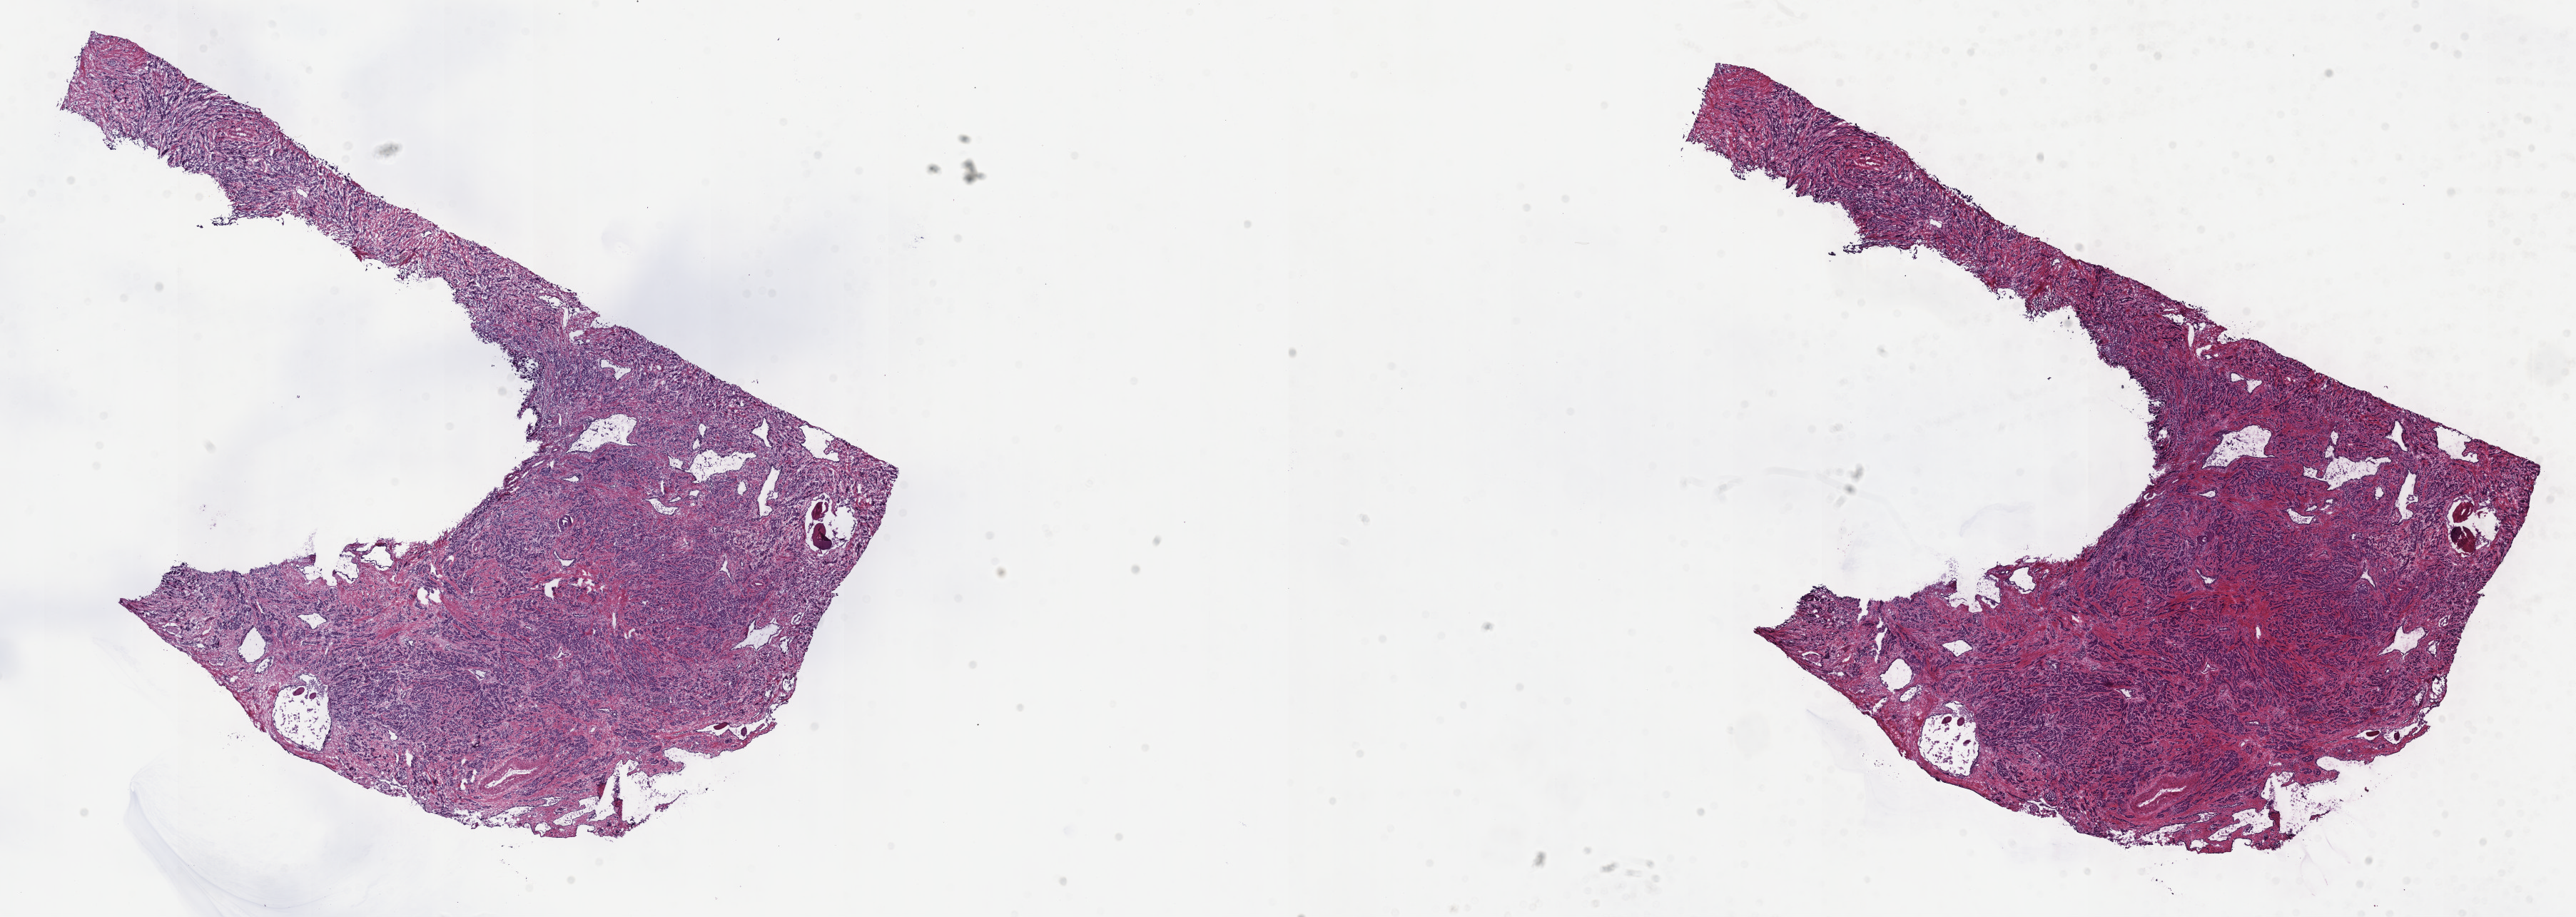
Whole-slide histology image, H&E-stained — whole scanned area (about 29.2 x 10.4 mm, from a 40x scan) shown as a low-resolution overview, frozen section from the top of the tissue portion, primary tumour sample from the prostate. Patient: male, age at initial diagnosis 62 years. Gleason score: 8 (4+4). Pathologist review of this section (percent, as recorded): tumour cells 95%, tumour nuclei 70%, normal cells 5%, stromal cells 0%, necrosis 0%. Infiltration values recorded for this section: lymphocyte infiltration 0%, monocyte infiltration 0%, neutrophil infiltration 0%.
Diagnosis: Adenocarcinoma, NOS. Laterality: bilateral.